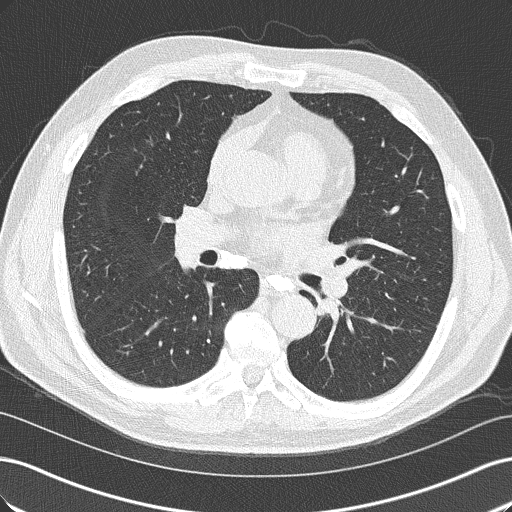
Low-dose screening chest CT, axial slice. Baseline annual screen. Lung window (W 1500 / L -600 HU). 2 mm slice thickness. Lung (sharp) reconstruction kernel (B50f). Slice 81 of 152 in the series. 512 × 512 image matrix, field of view 360 × 360 mm. Male, age 57 years at enrolment. Former smoker at enrolment.
• Expert-annotated lung lesion, bounding box [x1, y1, x2, y2] px = [301, 285, 360, 341].
• Screening reader's record for this exam: no non-calcified nodule ≥4 mm recorded.
• Participant outcome: lung cancer diagnosed 363 days after this screen — squamous cell carcinoma, NOS, left lower lobe, moderately differentiated (G2), stage IIIB (AJCC 6th edition), 38 mm at pathology.